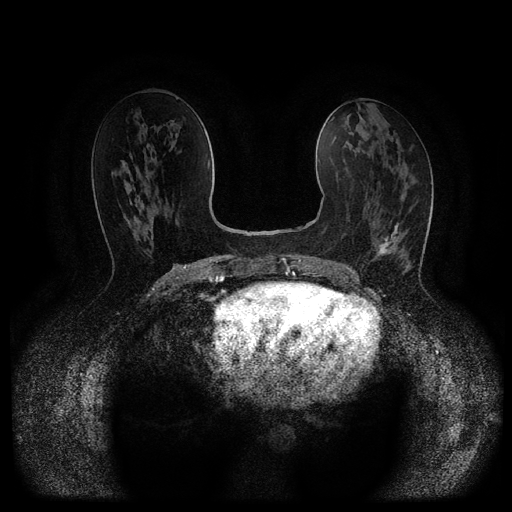
Breast MRI (dynamic contrast-enhanced, multi-phase), one axial slice; slice 47 of 116 in the series (ordered by position); dynamic contrast-enhanced series, time point 2 of 5 at this slice position (early post-contrast); 1.5 T; TE 2.6 ms, TR 5.4 ms; 512 × 512 image matrix, field of view 340 × 340 mm. Female patient, age 61 years.
Structures marked on this image (semi-automatic segmentation, software-assisted and operator-edited):
- breast lesion (labelled 'tumour' in the annotation; benign lesions carry a separate 'benign' label): box from (x=374, y=223) to (x=399, y=258) px